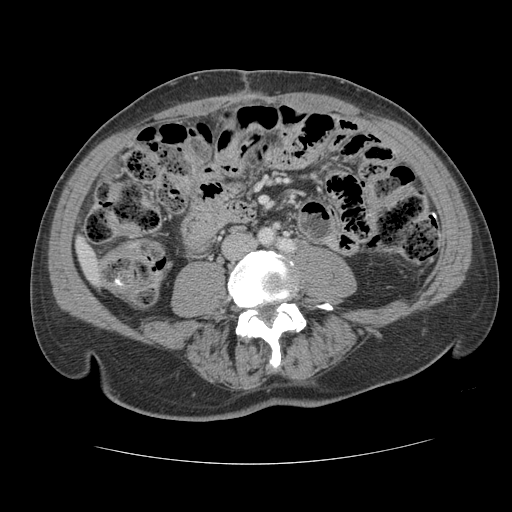
Contrast-enhanced abdominal CT, one axial slice. Slice 18 of 134 in the series (ordered by position). Reconstruction kernel STANDARD. 120 kVp. Soft-tissue window (W 400 / L 40 HU). 512 × 512 image matrix, field of view 377 × 377 mm. Male patient, age 68 years. From the clinical record (not read from this slice): diagnosis: colorectal cancer liver metastases, imaged before liver resection; multiple liver metastases: yes; largest metastasis: 2.2 cm; disease in both lobes: no.
Structures marked on this image (outlined manually by an expert reader):
- liver: bounding box (x1, y1, x2, y2) in pixels: (79, 243, 91, 270)
- planned liver remnant (the part of the liver to remain after resection): (79, 243, 91, 270)